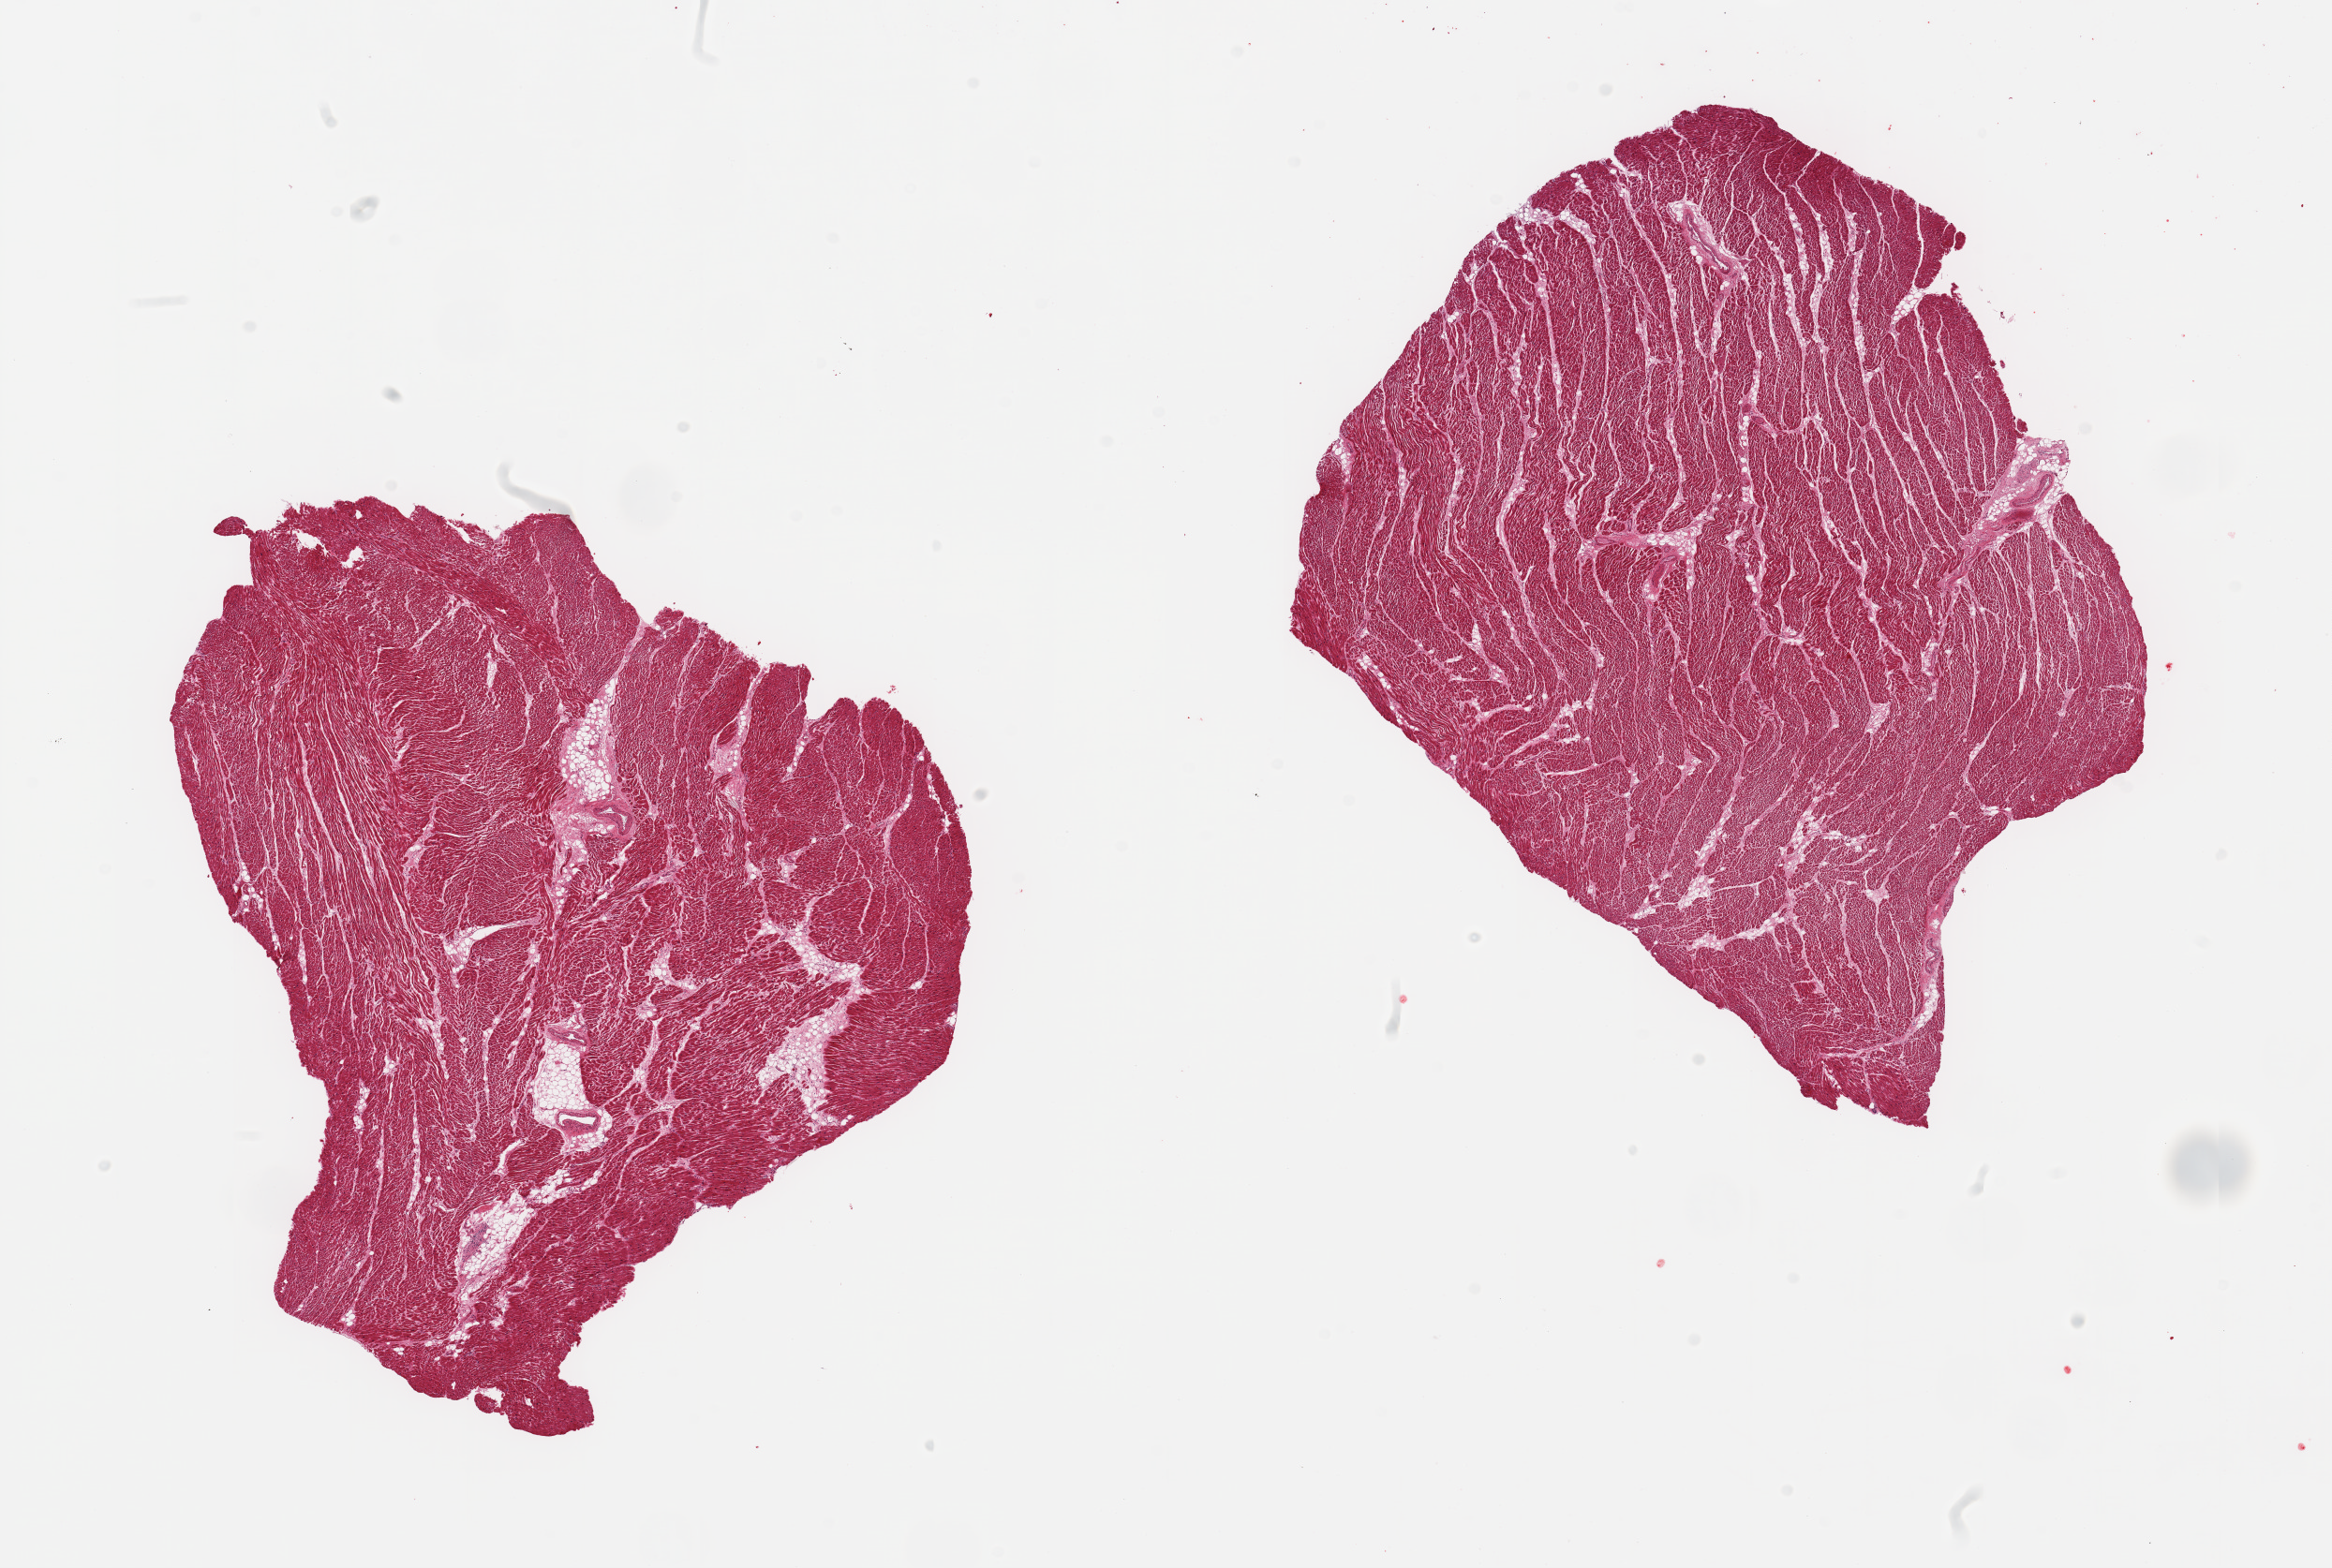
Digitized hematoxylin and eosin (H&E)-stained section, brightfield, low-resolution overview of the scanned area, about 19.7 x 13.2 mm (acquisition: 20x scan), PAXgene-fixed paraffin-embedded (PFPE) section, section of heart (target tissue), donor tissue sample.
* reviewer comment on this tissue sample: 2 pieces, mild diffuse chronic ischemic changes